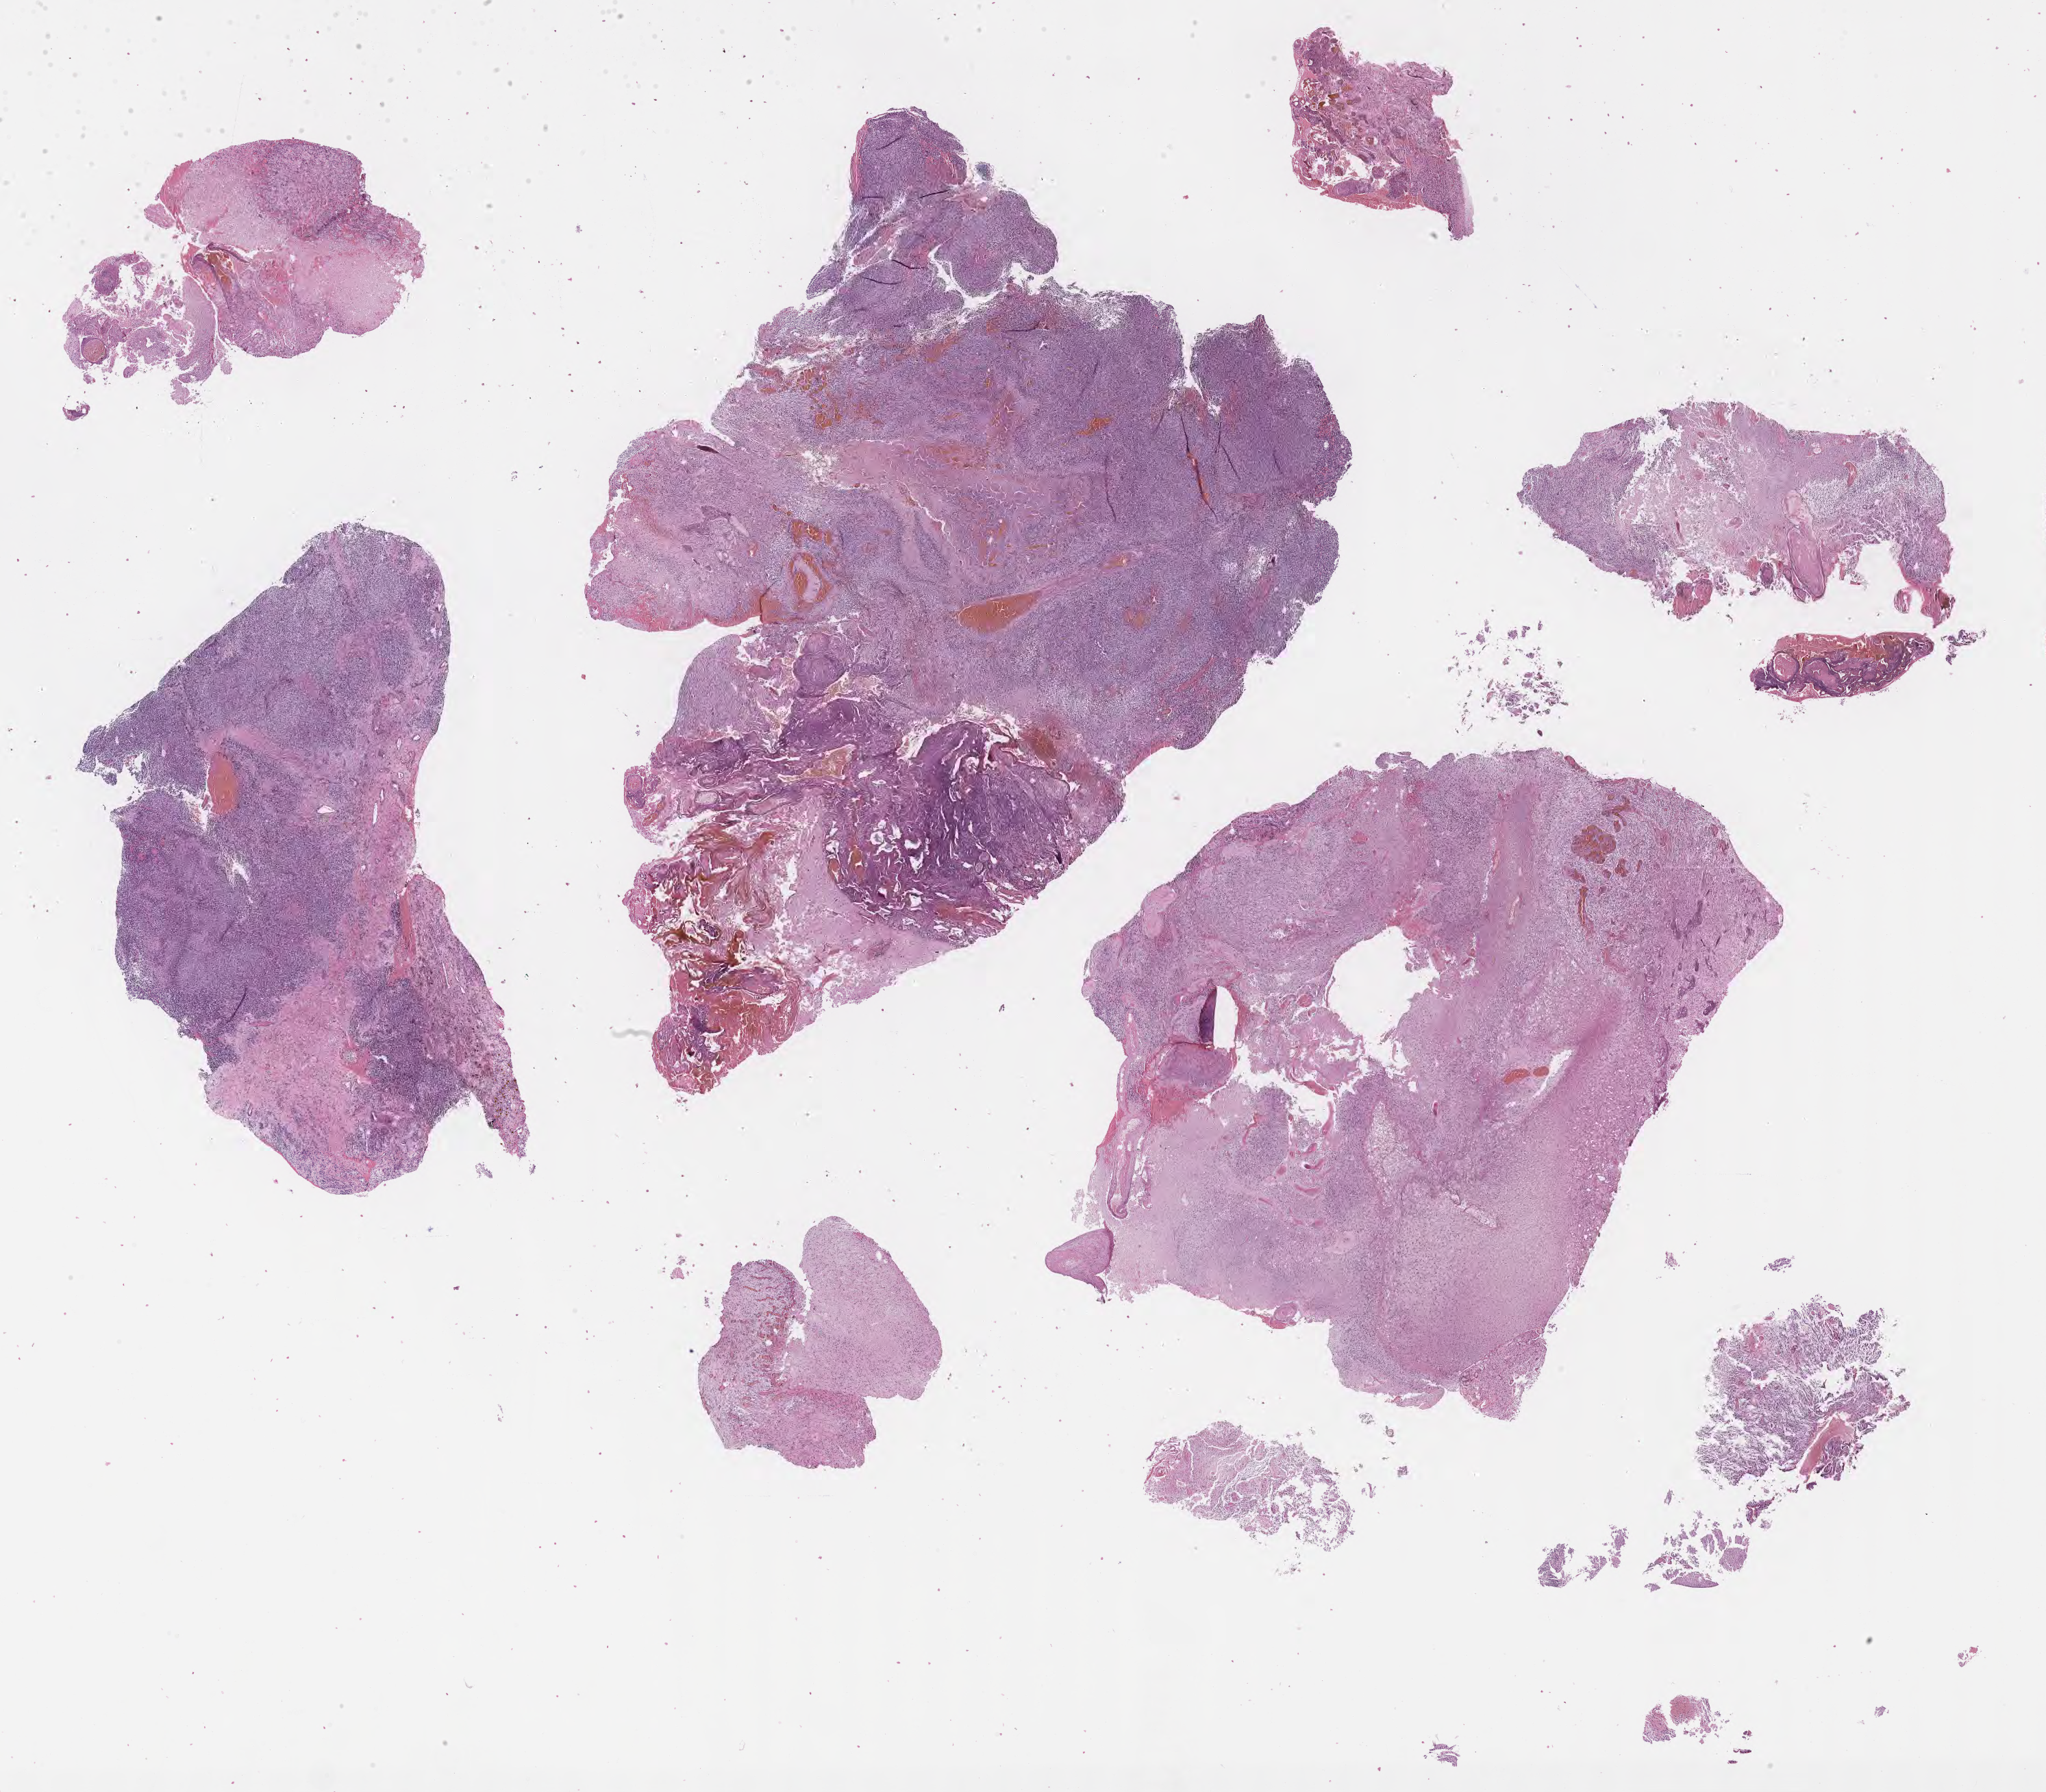
Whole-slide image, haematoxylin and eosin stain — low-resolution overview of the scanned area, about 24.2 x 21.2 mm. Formalin-fixed paraffin-embedded section. Specimen: primary tumor. Anatomic site: brain. Male, age 66 years at initial diagnosis. Composition of this section per pathologist review: tumor cells 61%, tumor nuclei 77%, stromal cells 9%, necrosis 12%, normal cells 18%. Infiltration values recorded for this section: lymphocyte infiltration 1%, monocyte infiltration 1%, neutrophil infiltration 1%.
- section: bottom of the tissue portion
- histologic diagnosis: Glioblastoma, NOS